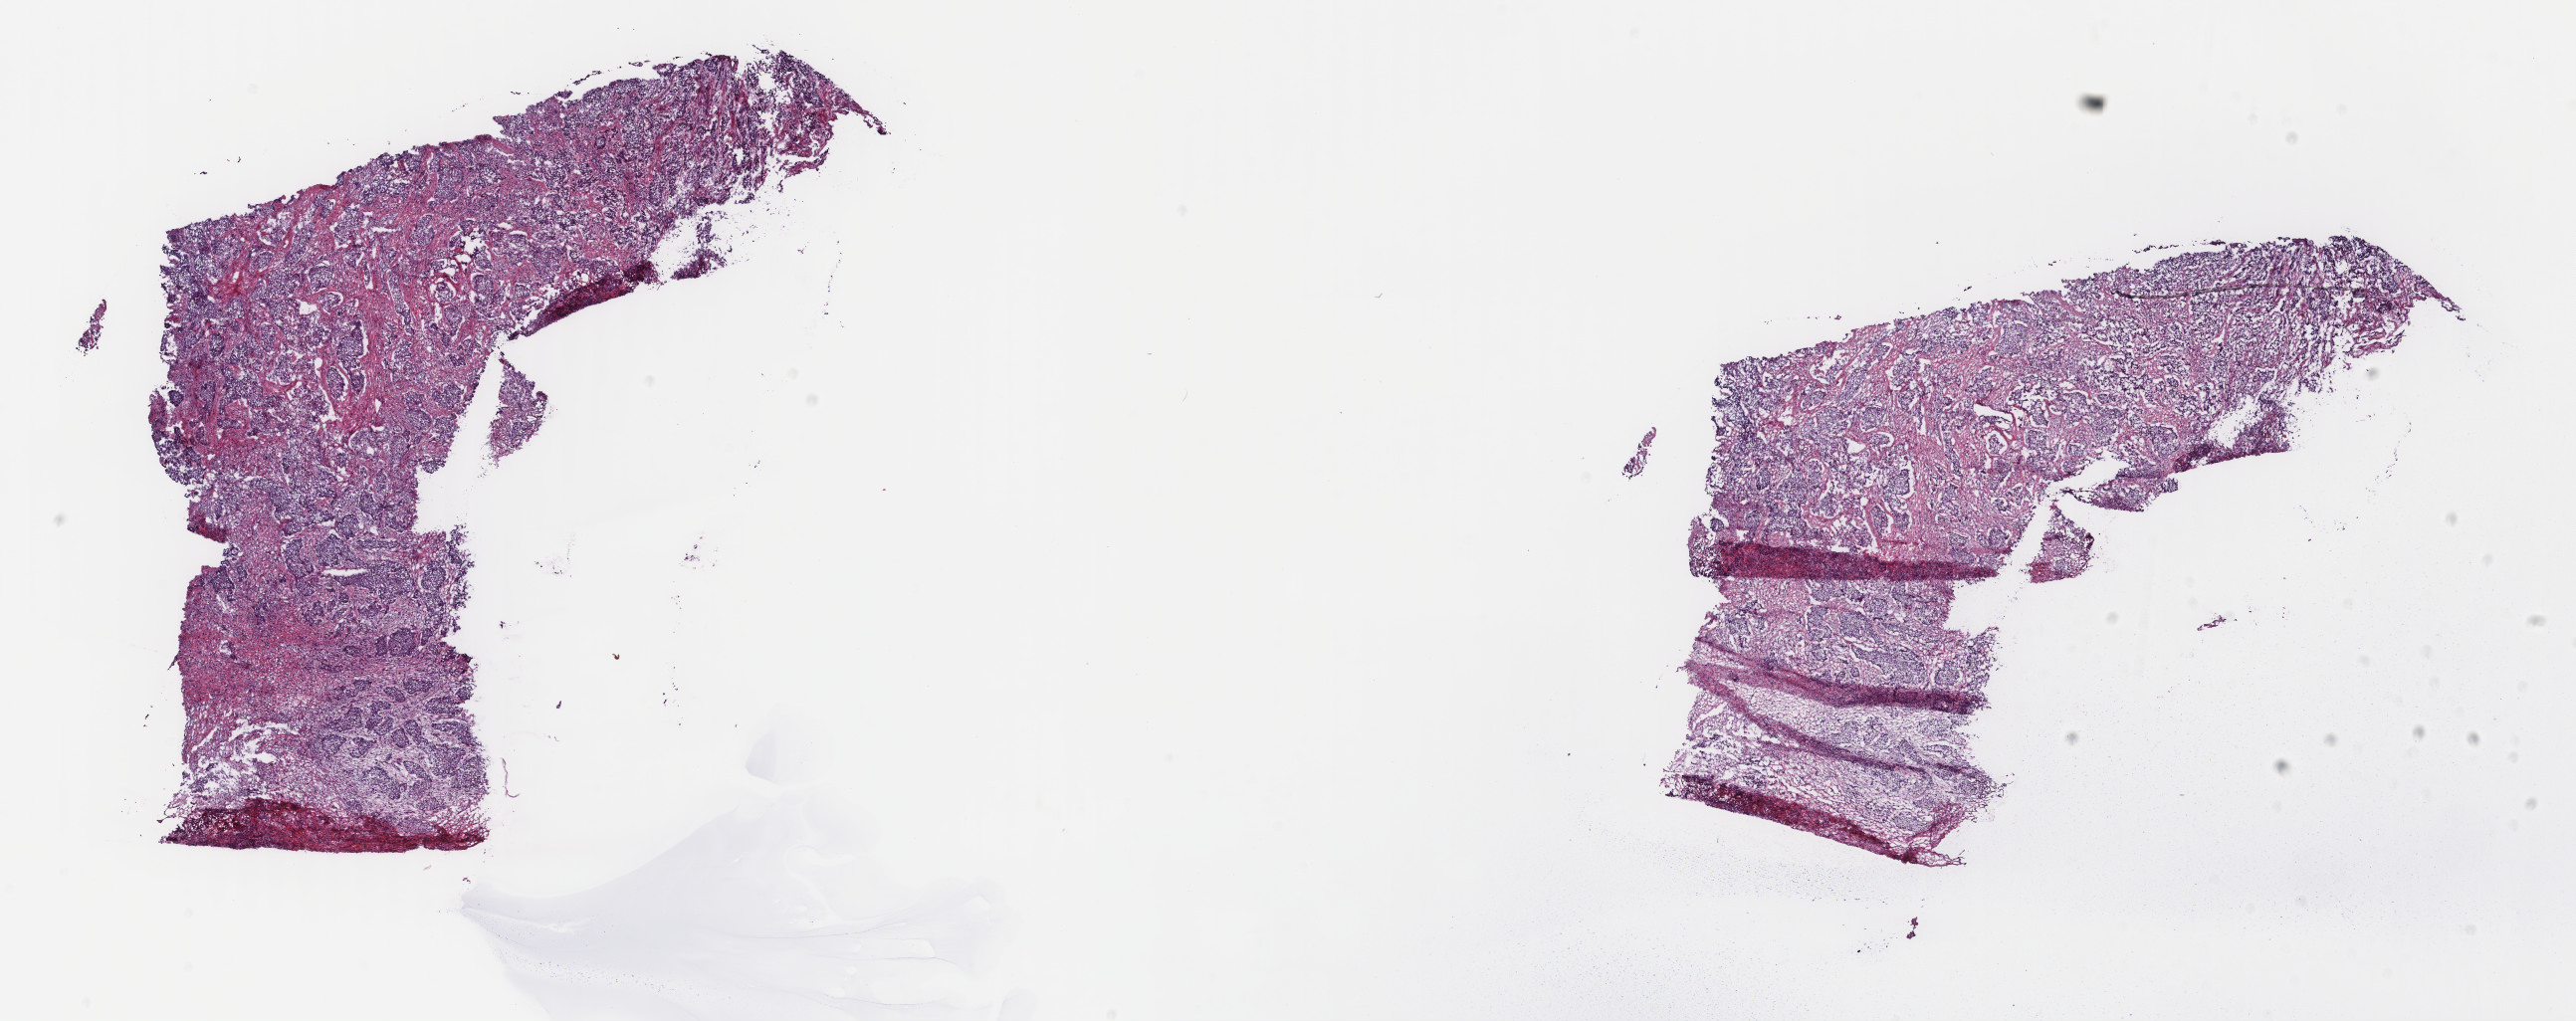
H&E-stained whole-slide image, whole scanned area (about 20.5 x 8.1 mm) shown as a low-resolution overview; frozen section from the top of the tissue portion; sample: primary tumour, cervix. Patient: female, age at initial diagnosis 75 years. Histologic grade: G3 (poorly differentiated). Pathologist review of this section (percent, as recorded): tumour cells 70%, tumour nuclei 70%, normal cells 0%, stromal cells 25%, necrosis 5%. Infiltration values recorded for this section: lymphocyte infiltration 40%, monocyte infiltration 10%, neutrophil infiltration 30%.
FIGO stage: IVA. Lymph nodes positive (case pathology): 0 of 19 examined. Diagnosis: Squamous cell carcinoma, NOS.